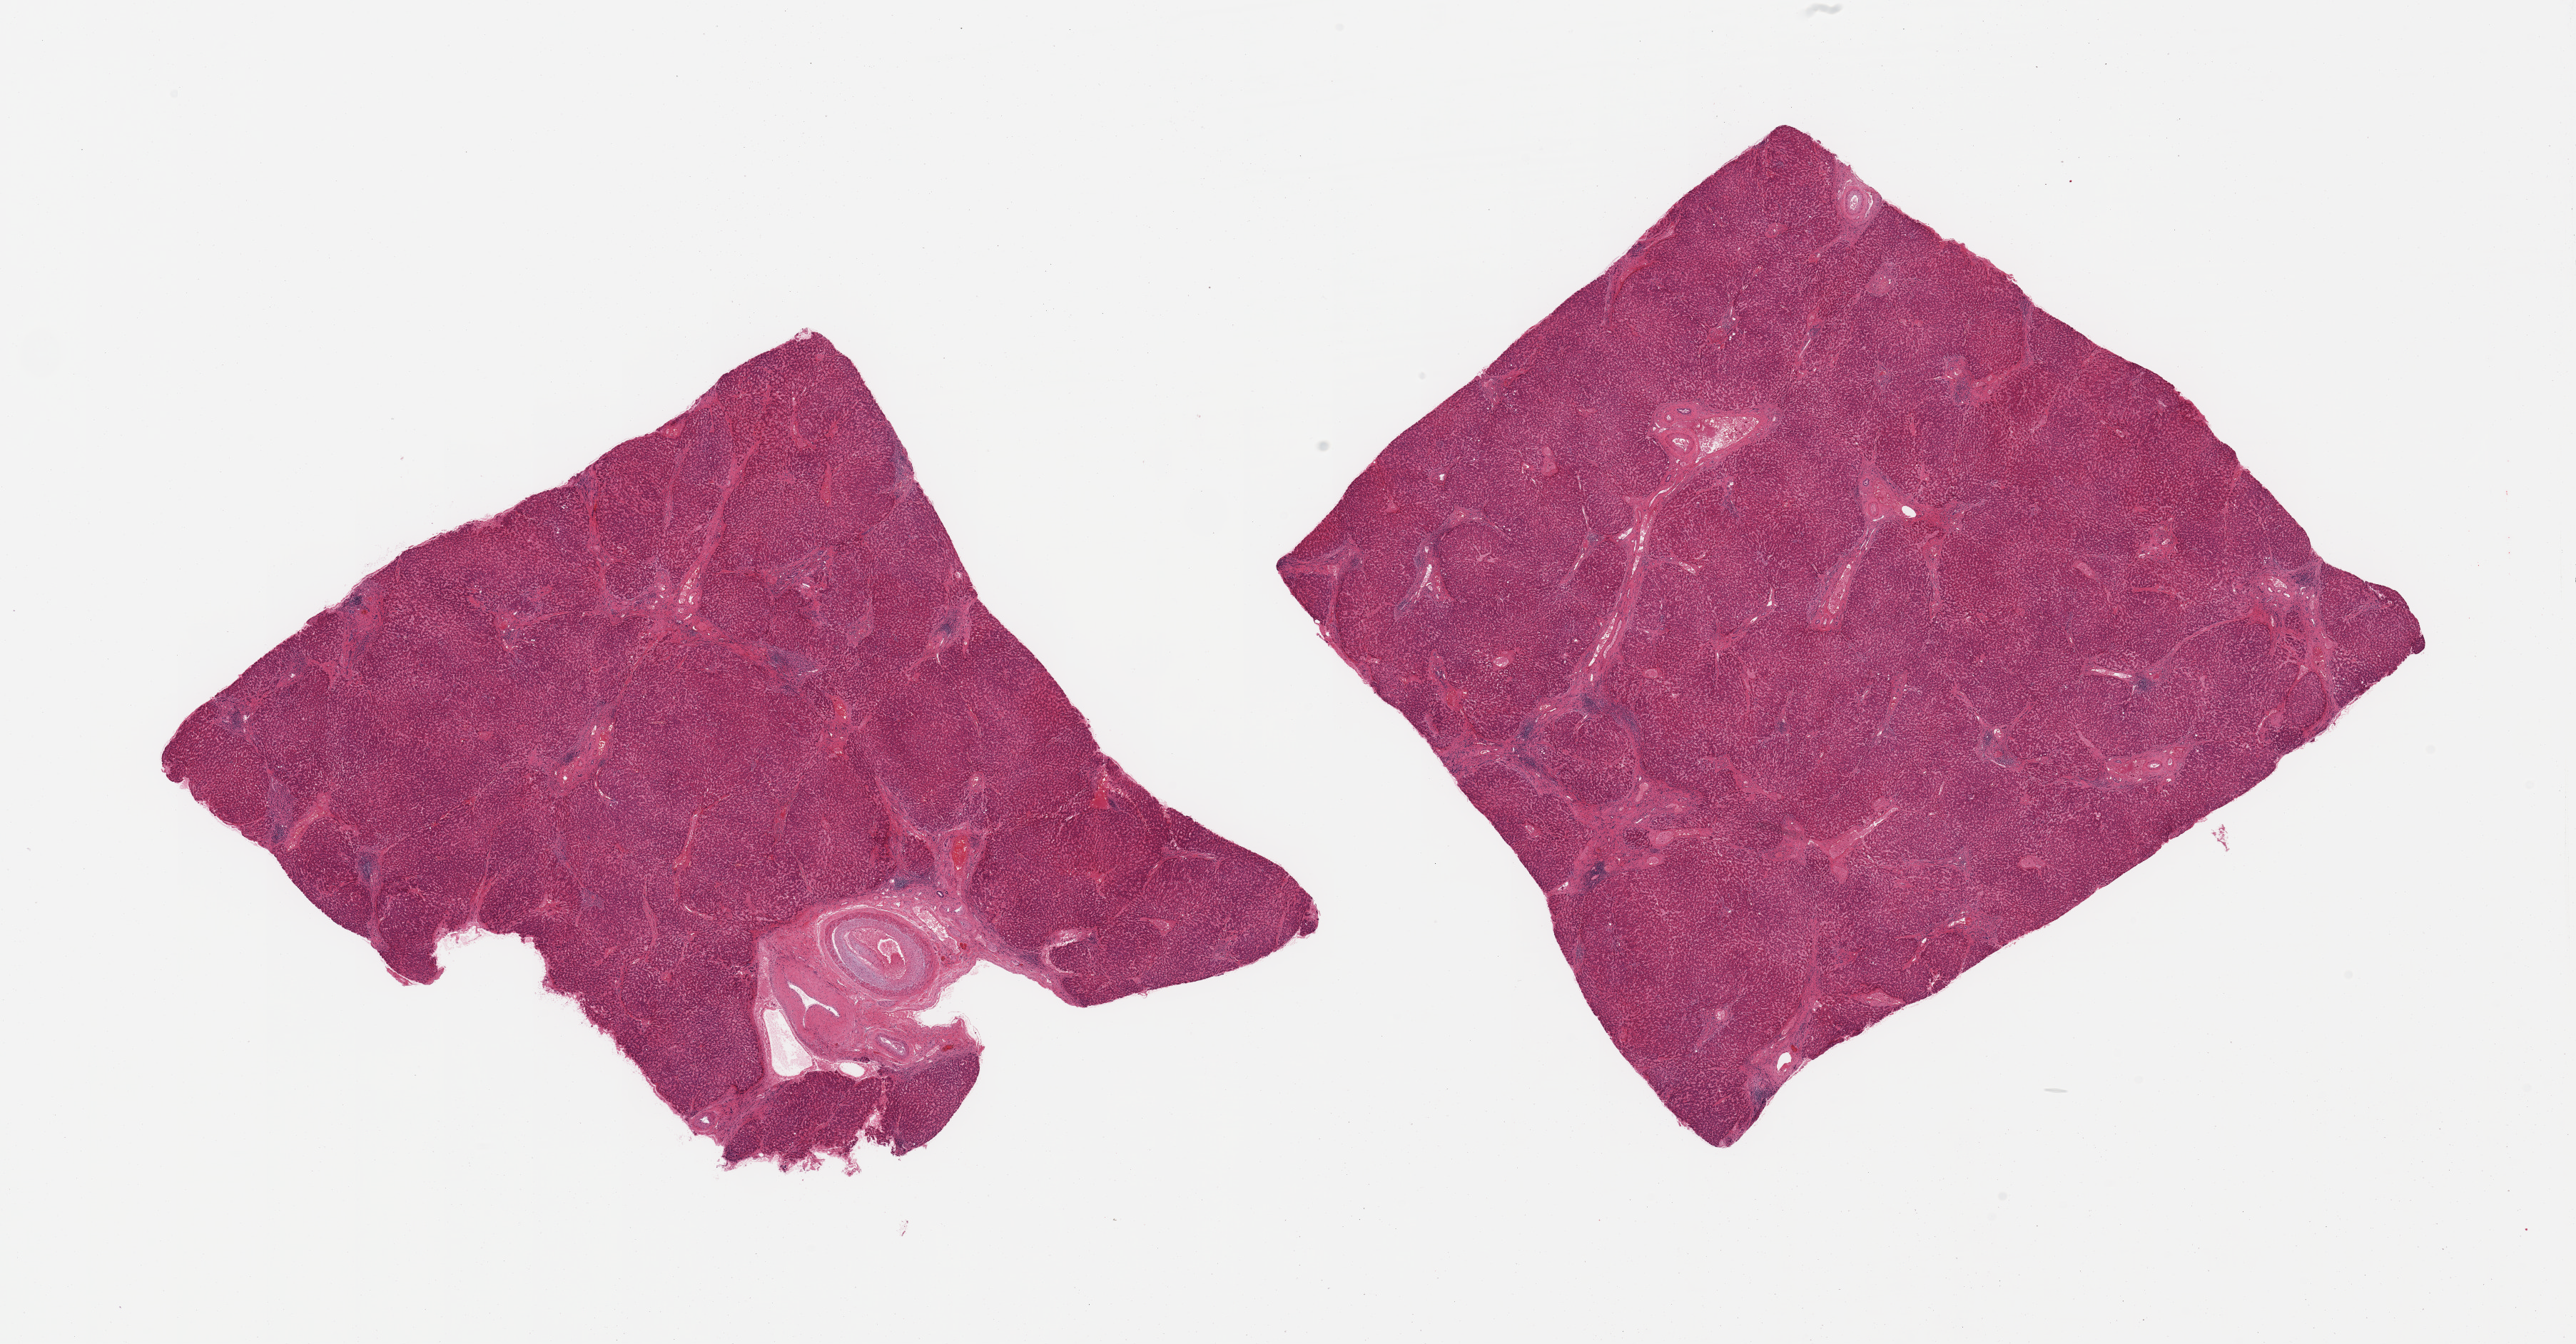
Whole-slide image, hematoxylin and eosin (H&E) stain, low-resolution overview of the scanned area, about 28.5 x 14.9 mm (from a 20x scan), PAXgene-fixed, paraffin-embedded tissue, target tissue: liver, donor tissue sample.
Reviewer comment on this tissue sample: 2 pieces; expanded portal areas with bile duct proliferation, lymphocytic infiltration and fibrosis with bridging consistent with cirrhosis; congestion; one piece contains large and thick walled vessels.